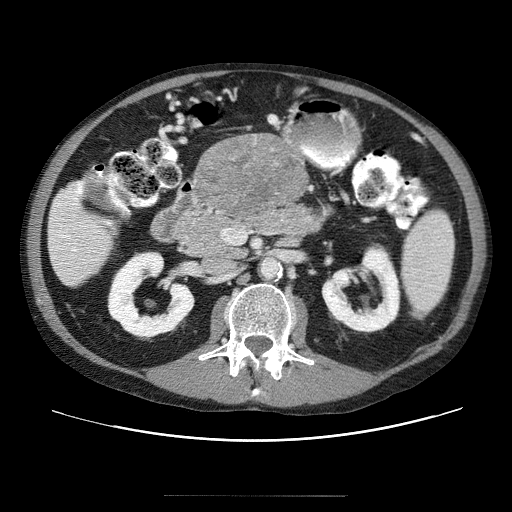
Contrast-enhanced abdominal CT (liver protocol), one axial slice. Position 7 of 69 along the scan axis. 120 kVp. Soft-tissue window (W 400 / L 40 HU). 512 × 512 image matrix, field of view 380 × 380 mm. From the clinical record (not read from this slice): diagnosis: hepatocellular carcinoma (patient treated with transarterial chemoembolisation; whether this scan precedes or follows treatment is not stated here); TNM stage (as recorded): Stage-IVB; Child-Pugh class: B; tumour differentiation: poorly differentiated.
Outlined on this slice (semi-automatically segmented with operator editing):
- liver parenchyma outside the tumour (the mass and vessels are separate outlines, so this box may not span the whole liver): box from (x=48, y=138) to (x=304, y=282) px
- mass: (x=192, y=133)–(x=311, y=220)
- liver vessels: (x=56, y=211)–(x=97, y=273)